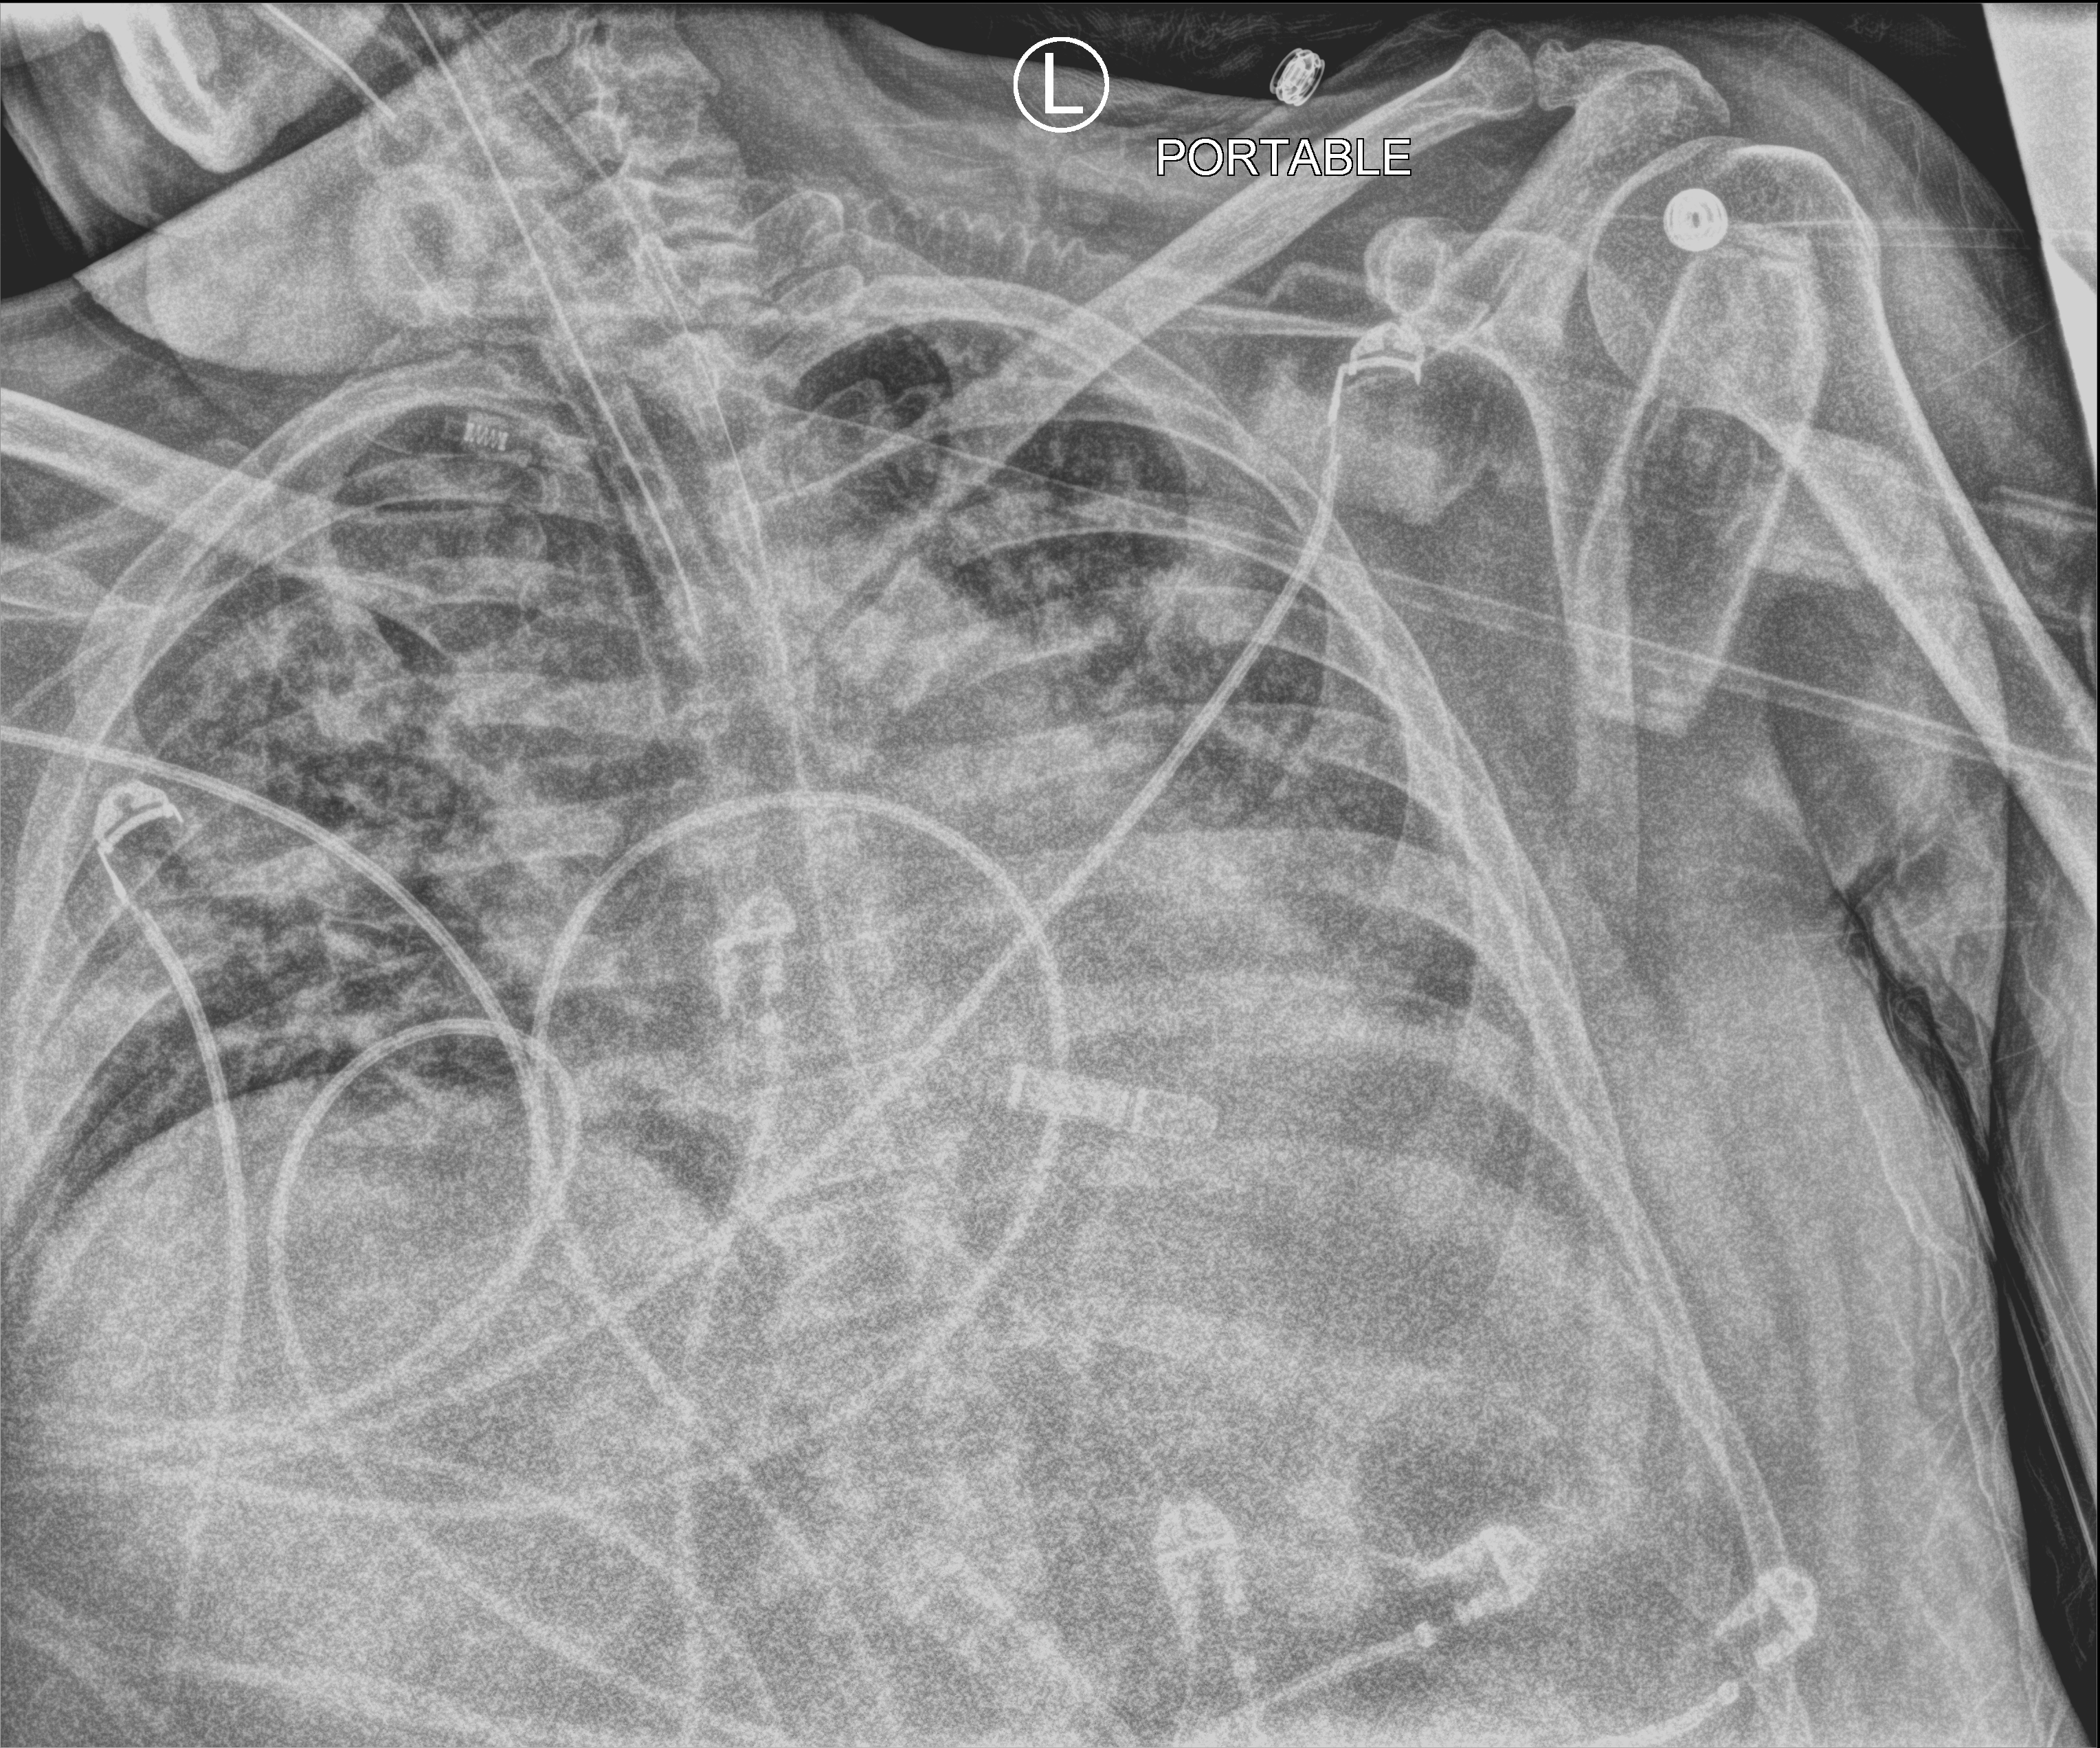
Chest X-ray (portable), anteroposterior (AP) projection. Male patient hospitalised with COVID-19, age 18–59 years.
Hospital-stay facts (about this admission, not read from this image; timing relative to this image not recorded): admitted to intensive care during this hospital stay: yes; mechanically ventilated during this hospital stay: yes.